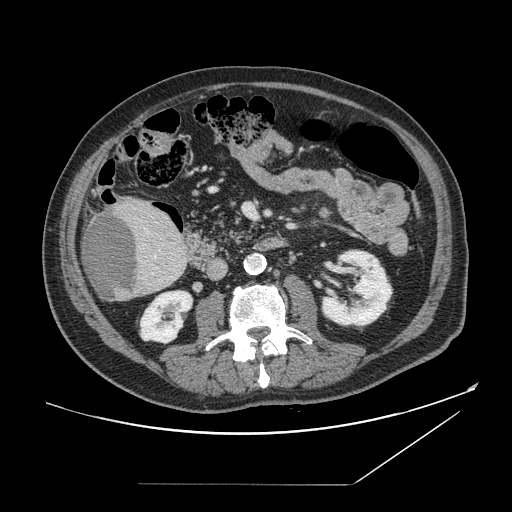
Contrast-enhanced abdominal CT, one axial slice; position 50 of 166 along the scan axis; intravenous contrast given; soft-tissue window (W 400 / L 40 HU); 2.5 mm slice thickness; 512 × 512 image matrix. Male patient, age 80 years. Case-level facts recorded for this patient, not image findings: diagnosis: colorectal cancer liver metastases, imaged before liver resection; multiple liver metastases: no; largest metastasis: 2.2 cm; chemotherapy before resection: no.
Annotated regions visible in this slice (manually delineated by an expert):
- liver: bounding box [x1, y1, x2, y2] px = [82, 198, 188, 302]
- liver metastasis: [82, 212, 138, 301]